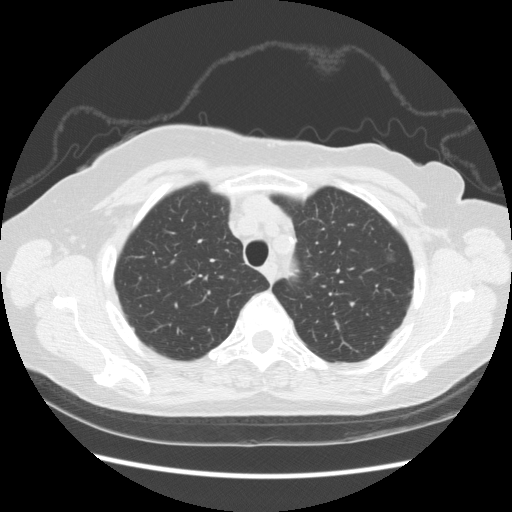
Axial slice from a low-dose chest CT screening exam. First (baseline) screen. Lung window (W 1500 / L -600 HU). 2.5 mm slice thickness. Slice 38 of 247 in the series. 512 × 512 image matrix, field of view 360 × 360 mm. Female, age 73 years at enrolment.
Expert reader's lesion annotation, box from (x=373, y=229) to (x=417, y=274) px. The screening reader recorded 3 non-calcified nodules or masses ≥4 mm on this exam; which of them this box marks is not recorded.